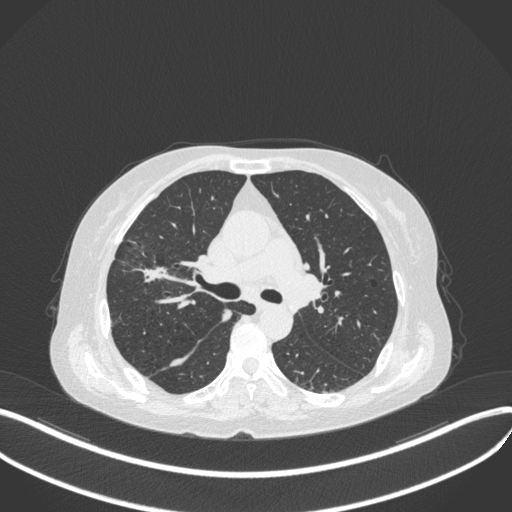
Chest CT, one axial slice. Slice 252 of 429 in the series (ordered by position). Reconstruction kernel B31f. Lung window (W 1500 / L -600 HU). 1 mm slice thickness. 512 × 512 image matrix, field of view 400 × 400 mm. Patient: female, 69 years. From the clinical record (not read from this slice): clinical TNM (as recorded): T1b N3 M0.
Outlined on this slice (rectangle marked by the reading radiologist):
- lung tumour (recorded histology: small cell carcinoma): box from (x=130, y=261) to (x=183, y=286) px